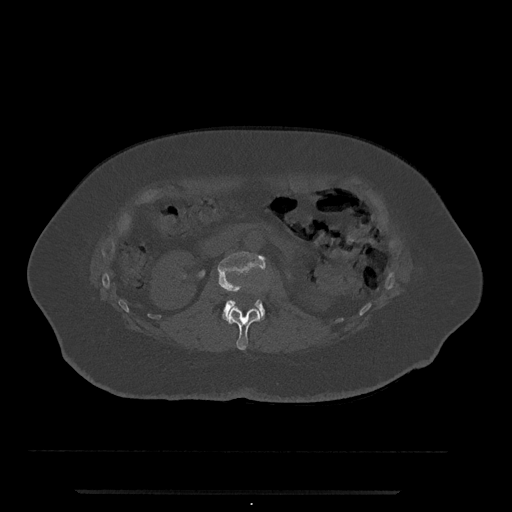
CT including the spine, one axial slice. Position 69 of 797 along the scan axis. 120 kVp. Bone window (W 1800 / L 400 HU). 512 × 512 image matrix. Female patient, age 51 years. From the clinical record (not read from this slice): primary cancer: neuro.
Structures marked on this image (semi-automatically segmented with operator editing):
- L1 vertebra: bounding box (x1, y1, x2, y2) in pixels: (225, 308, 262, 350)
- L2 vertebra: (218, 251, 265, 320)